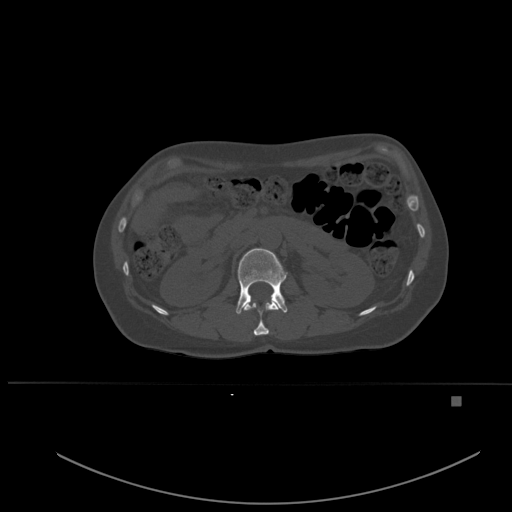
CT including the spine, one axial slice; position 240 of 651 along the scan axis; bone window (W 1800 / L 400 HU); 512 × 512 image matrix, field of view 443 × 443 mm. Patient: female, 49 years. Case-level facts recorded for this patient, not image findings: primary cancer: breast.
Annotated regions visible in this slice (semi-automatically segmented with operator editing):
- L1 vertebra: bounding box (x1, y1, x2, y2) in pixels: (236, 248, 288, 314)
- T12 vertebra: (243, 300, 280, 336)